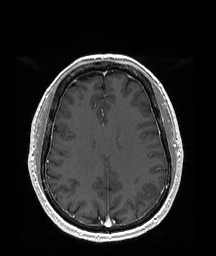
Brain MRI from a brain-tumour surgery series, one axial slice; position 75 of 192 along the scan axis; T1-weighted post-contrast; 1 mm slice thickness; 216 × 256 image matrix, field of view 219 × 260 mm. From the clinical record (not read from this slice): histopathology: Glioblastoma; WHO grade: 4; IDH mutation: no.
Structures marked on this image (expert manual segmentation):
- tumour: bounding box [x1, y1, x2, y2] px = [143, 182, 162, 207]